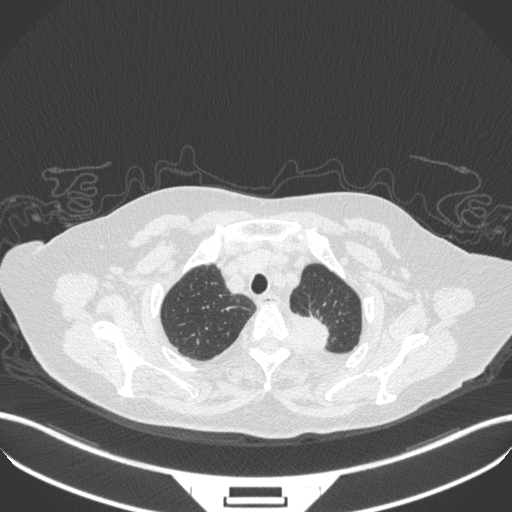
Chest CT, one axial slice; slice 298 of 353 in the series (ordered by position); reconstruction kernel B31f; 100 kVp; lung window (W 1500 / L -600 HU); 1 mm slice thickness; 512 × 512 image matrix, field of view 400 × 400 mm. Female patient, age 81 years. From the clinical record (not read from this slice): clinical TNM (as recorded): T2a N0 M0.
Annotated regions visible in this slice (rectangle marked by the reading radiologist):
- lung tumour (recorded histology: adenocarcinoma): box from (x=285, y=306) to (x=333, y=353) px